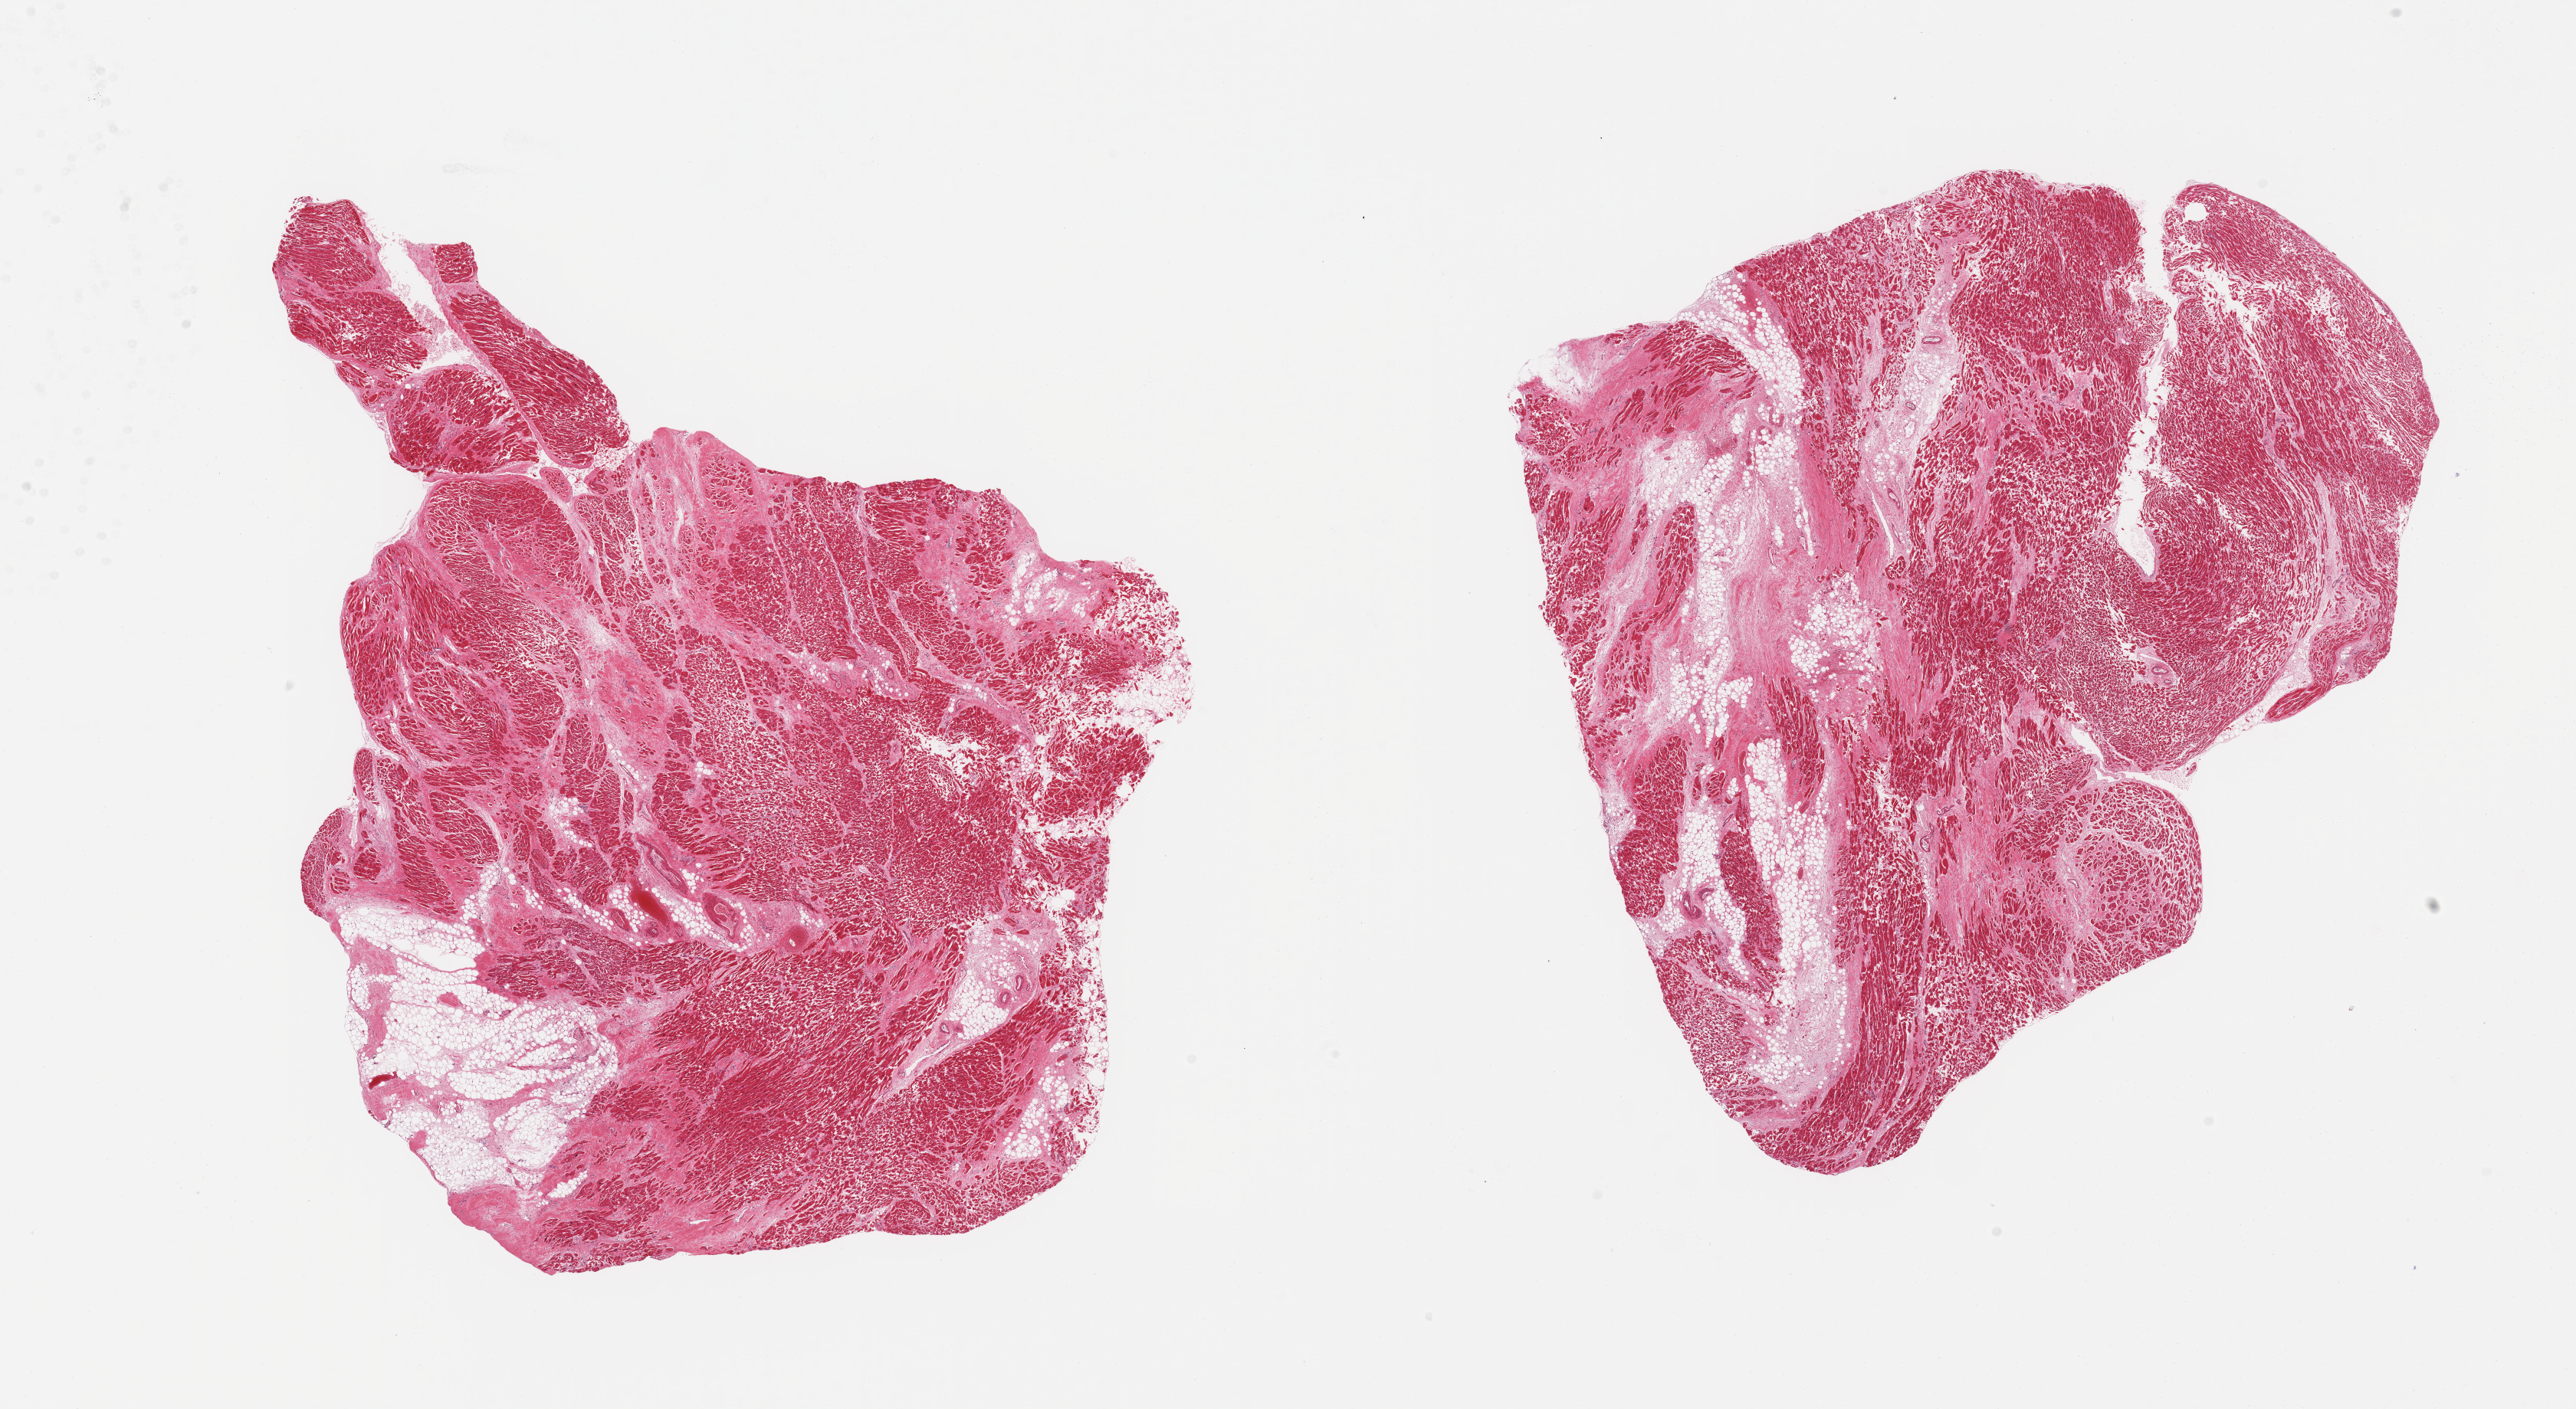
H&E whole-slide image, brightfield, whole scanned area (about 26.6 x 14.5 mm) shown as a low-resolution overview; PAXgene-fixed, paraffin-embedded tissue; sampled site (target tissue): heart; donor tissue sample.
• reviewer comment on this tissue sample: 2 pieces, severe interstitial fibrosis/chronic ischemic changes, remote infarcts